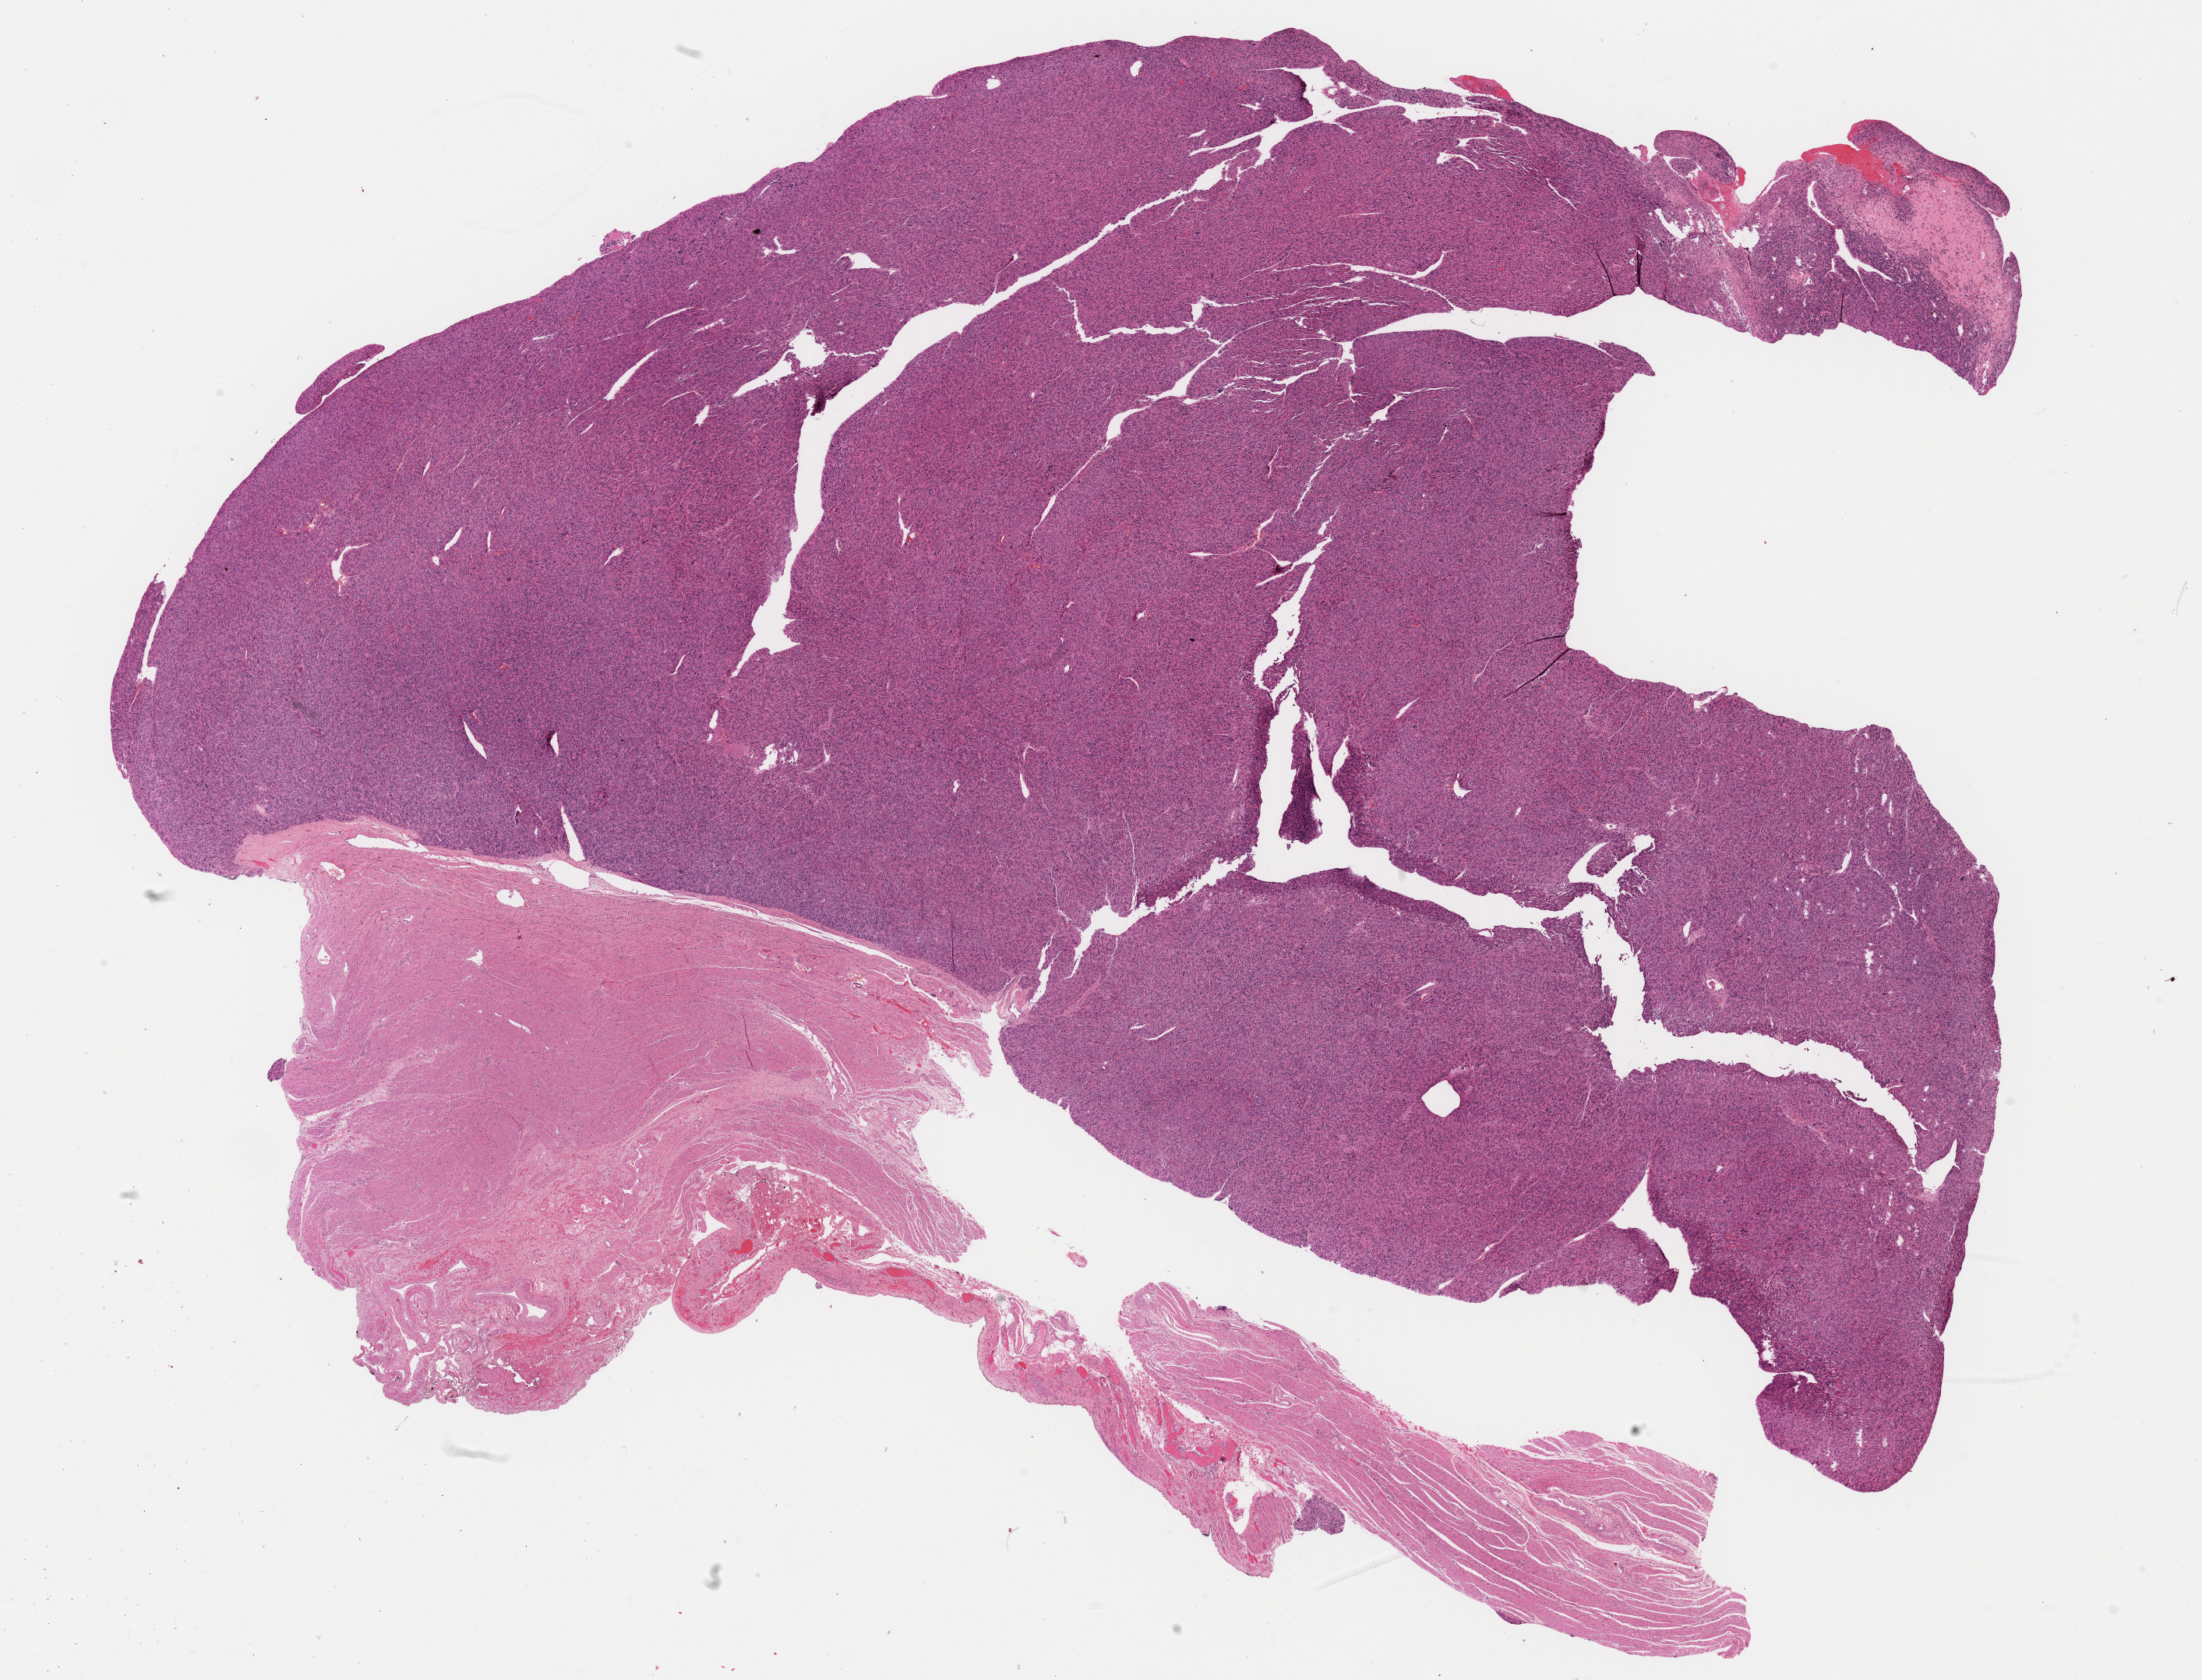
Whole-slide histology image, H&E-stained — low-resolution overview of the scanned area, about 22.3 x 17.0 mm, FFPE section, uterus, primary tumour sample. Female patient; age at initial diagnosis 60 years.
Histologic diagnosis: Leiomyosarcoma, NOS.